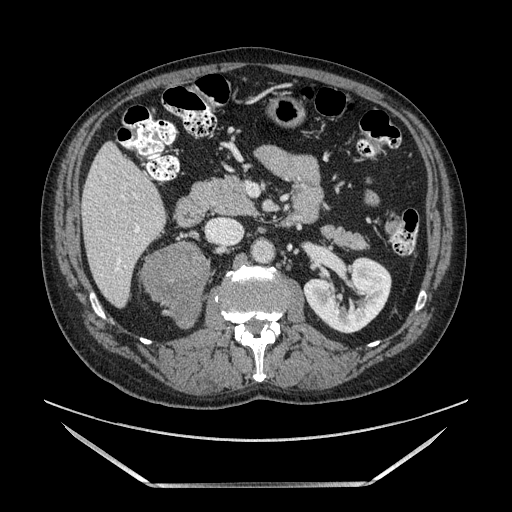
Contrast-enhanced abdominal CT, one axial slice. Position 56 of 185 along the scan axis. Soft-tissue window (W 400 / L 40 HU). 512 × 512 image matrix. Male patient. Case-level facts recorded for this patient, not image findings: diagnosis: adrenocortical carcinoma; tumour side: right adrenal; tumour size at pathology: 10.3 cm; Ki-67 index: 20 %; stage (as recorded): 3.
Outlined on this slice (semi-automatically segmented with operator editing):
- mass: bounding box <141,245,210,327> (left, top, right, bottom; pixels)